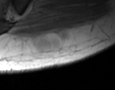
MRI of an extremity soft-tissue mass, one axial slice. Slice 11 of 35 in the series (ordered by position). MR volume resampled by the dataset authors to the PET/CT grid (not the native acquisition matrix). 115 × 90 image matrix, field of view 112 × 88 mm. Male patient. From the clinical record (not read from this slice): histological type: pleiomorphic leiomyosarcoma; grade: high; site of the primary tumour: left buttock.
Annotated regions visible in this slice (expert contour drawn on MRI and transferred to this co-registered scan by the dataset authors):
- gross tumour volume including surrounding oedema: bounding box (x1, y1, x2, y2) in pixels: (56, 32, 66, 47)
- gross tumour volume (mass): (58, 37, 65, 47)